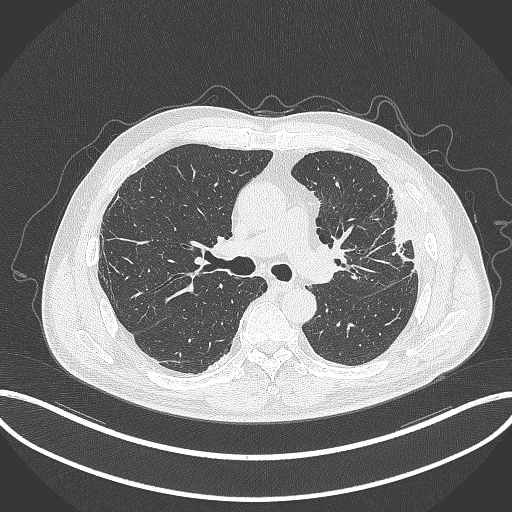
Chest CT, one axial slice. Lung window (W 1500 / L -600 HU). 1 mm slice thickness. 512 × 512 image matrix, field of view 415 × 415 mm. Male patient, age 64 years. Case-level facts recorded for this patient, not image findings: clinical TNM (as recorded): T4 N1 M0; histopathological grade: G3.
Annotated regions visible in this slice (bounding box drawn by a radiologist):
- lung tumour (recorded histology: adenocarcinoma): box from (x=375, y=189) to (x=421, y=268) px